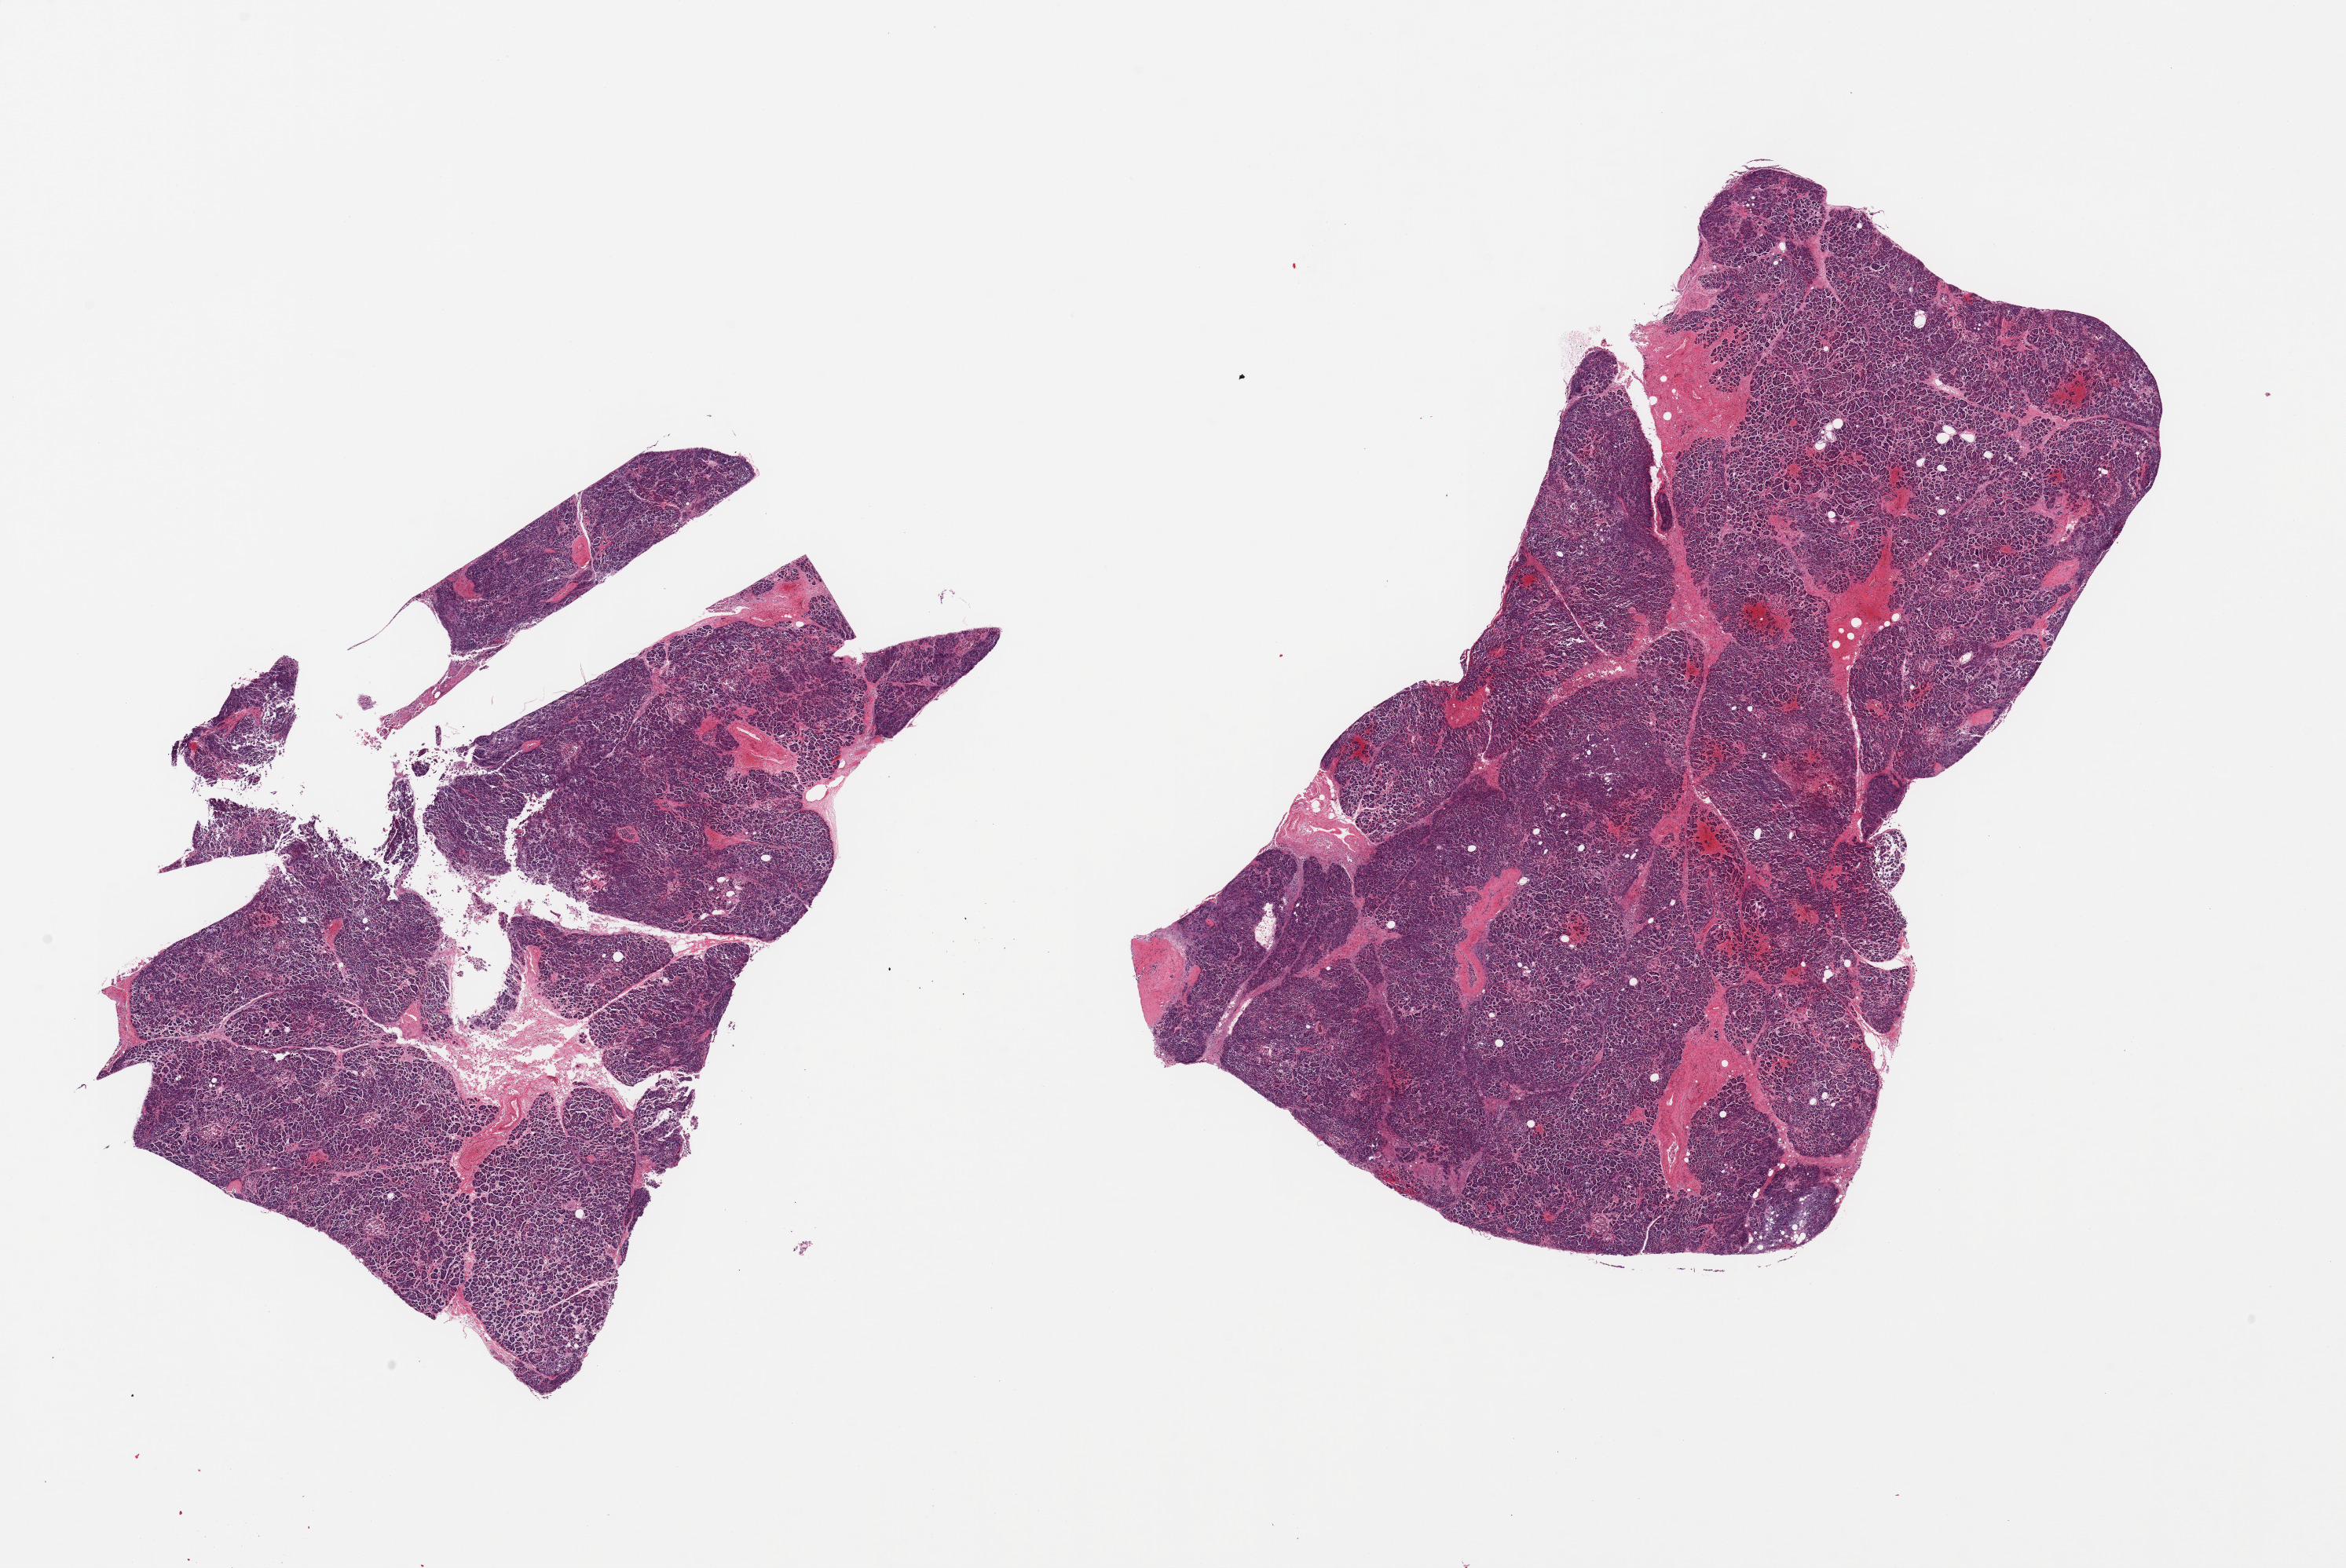
Haematoxylin and eosin whole-slide image, low-resolution overview of the scanned area, about 23.6 x 15.8 mm; PAXgene-fixed paraffin-embedded (PFPE) section; section of pancreas (target tissue); donor tissue sample. Donor sex: female.
Reviewer comment on this tissue sample: 2 pieces; <5% fat.